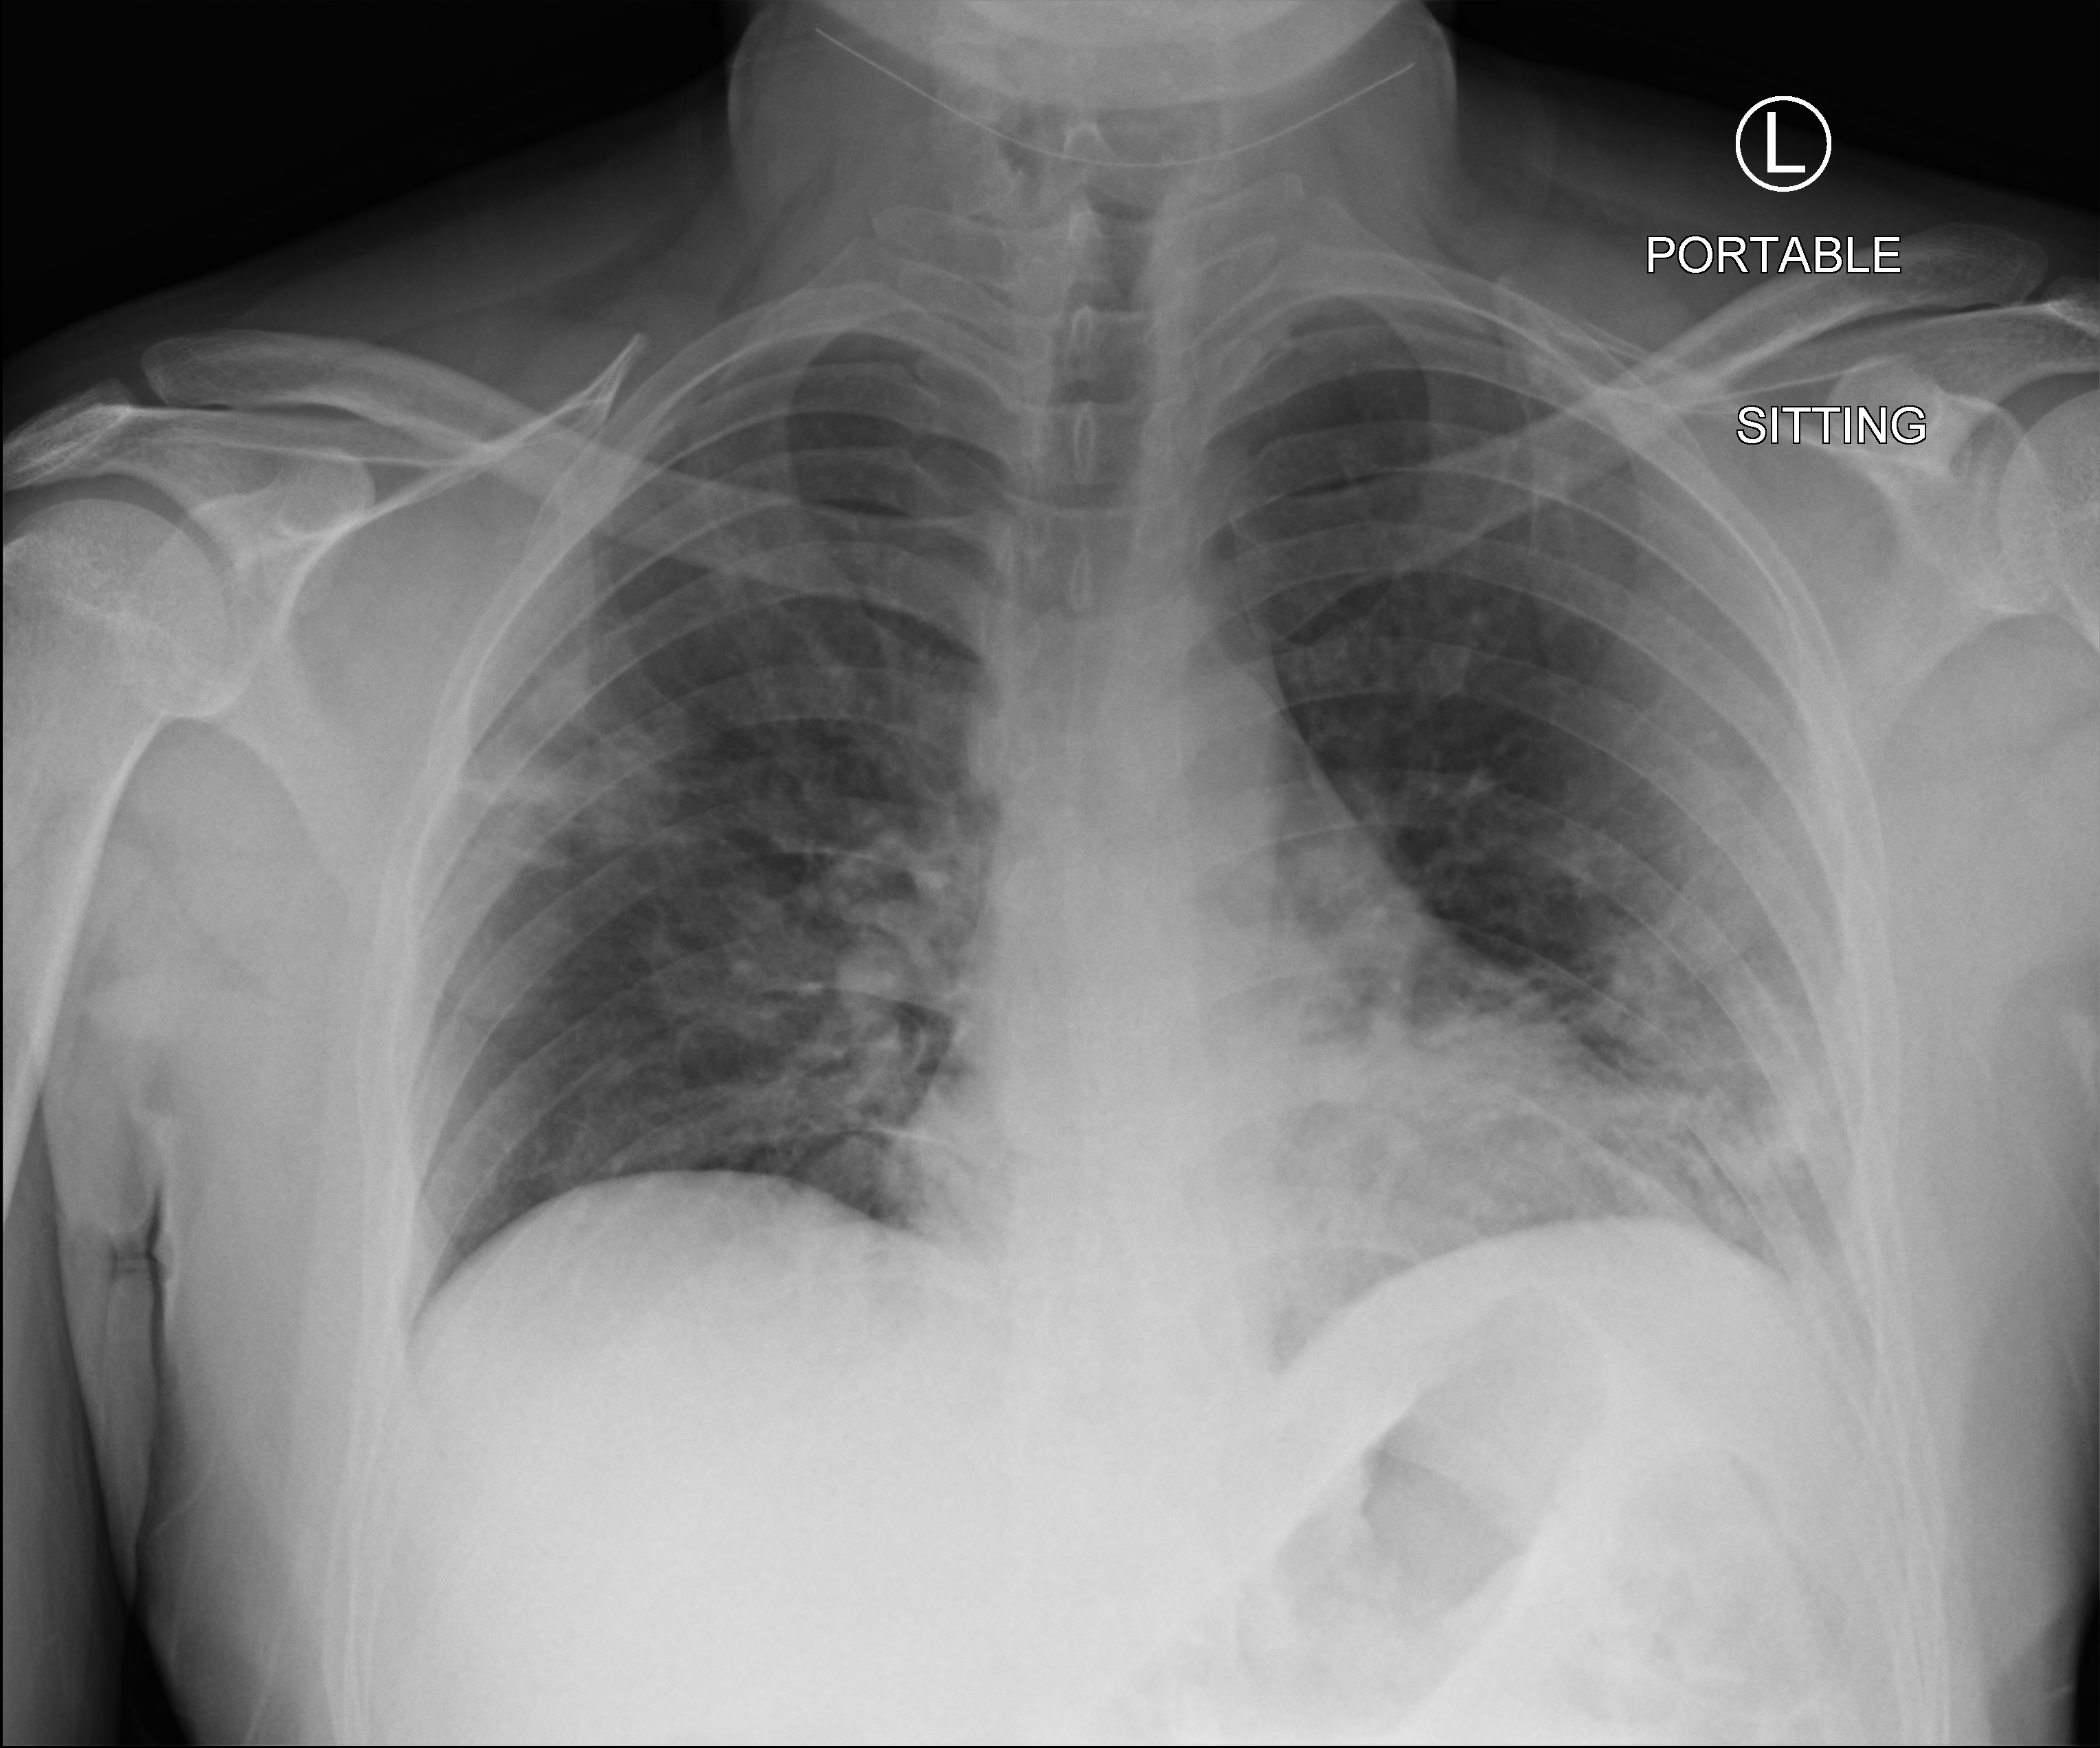
Bedside chest radiograph (computed radiography). Patient hospitalised with COVID-19; male, aged 18–59 years.
Hospital-stay facts (about this admission, not read from this image; timing relative to this image not recorded): hypertension (admission record): no; diabetes (admission record): no.